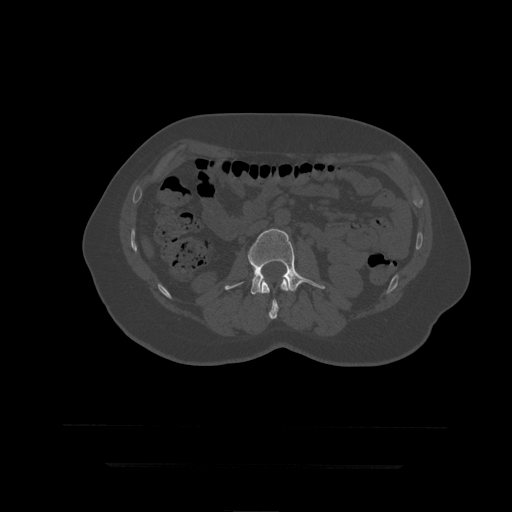
CT including the spine, one axial slice. Position 132 of 399 along the scan axis. Reconstruction kernel STANDARD. 120 kVp. Bone window (W 1800 / L 400 HU). 512 × 512 image matrix, field of view 450 × 450 mm. Patient age 41 years. Case-level facts recorded for this patient, not image findings: primary cancer: breast.
Annotated regions visible in this slice (semi-automatic segmentation, software-assisted and operator-edited):
- L2 vertebra: bounding box <261,278,289,320> (left, top, right, bottom; pixels)
- L3 vertebra: <225,229,326,295>